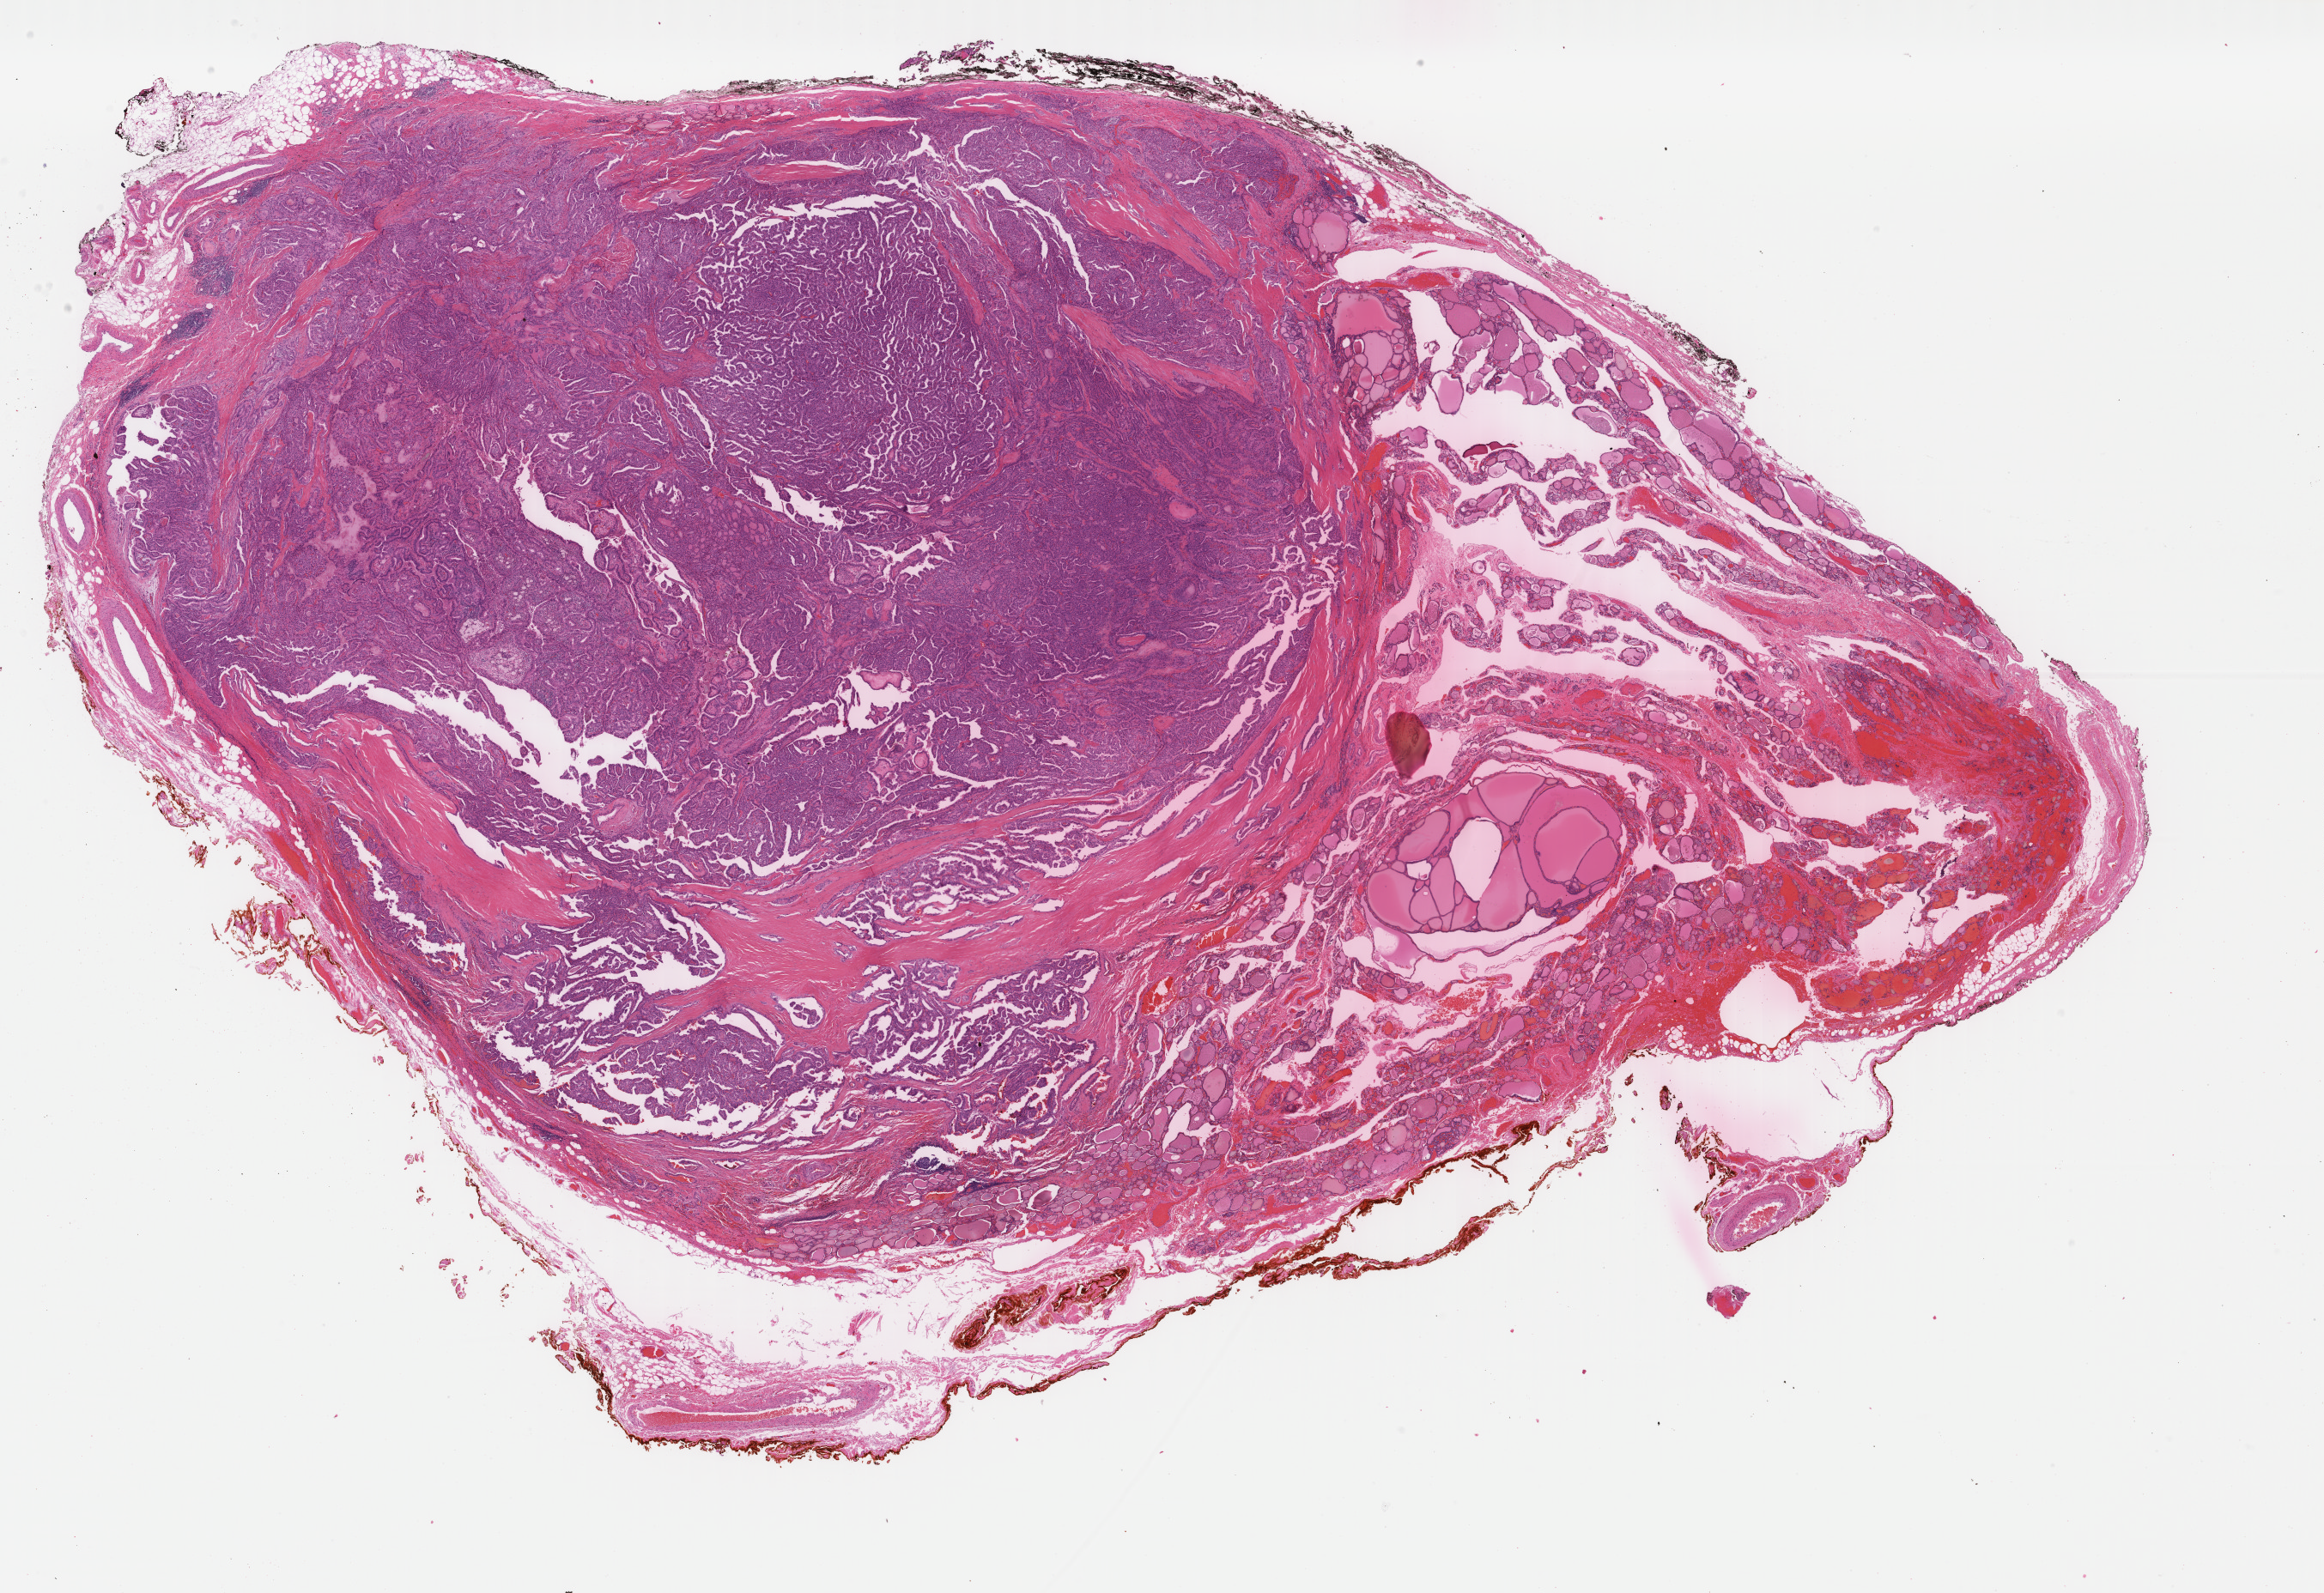
Whole-slide histology image, H&E — low-resolution overview of the scanned area, about 21.5 x 14.7 mm (acquisition: 40x scan). FFPE section. Primary tumour sample from the thyroid. Female patient; age at initial diagnosis 72 years.
AJCC pathologic stage: I. Diagnosis: Papillary adenocarcinoma, NOS.